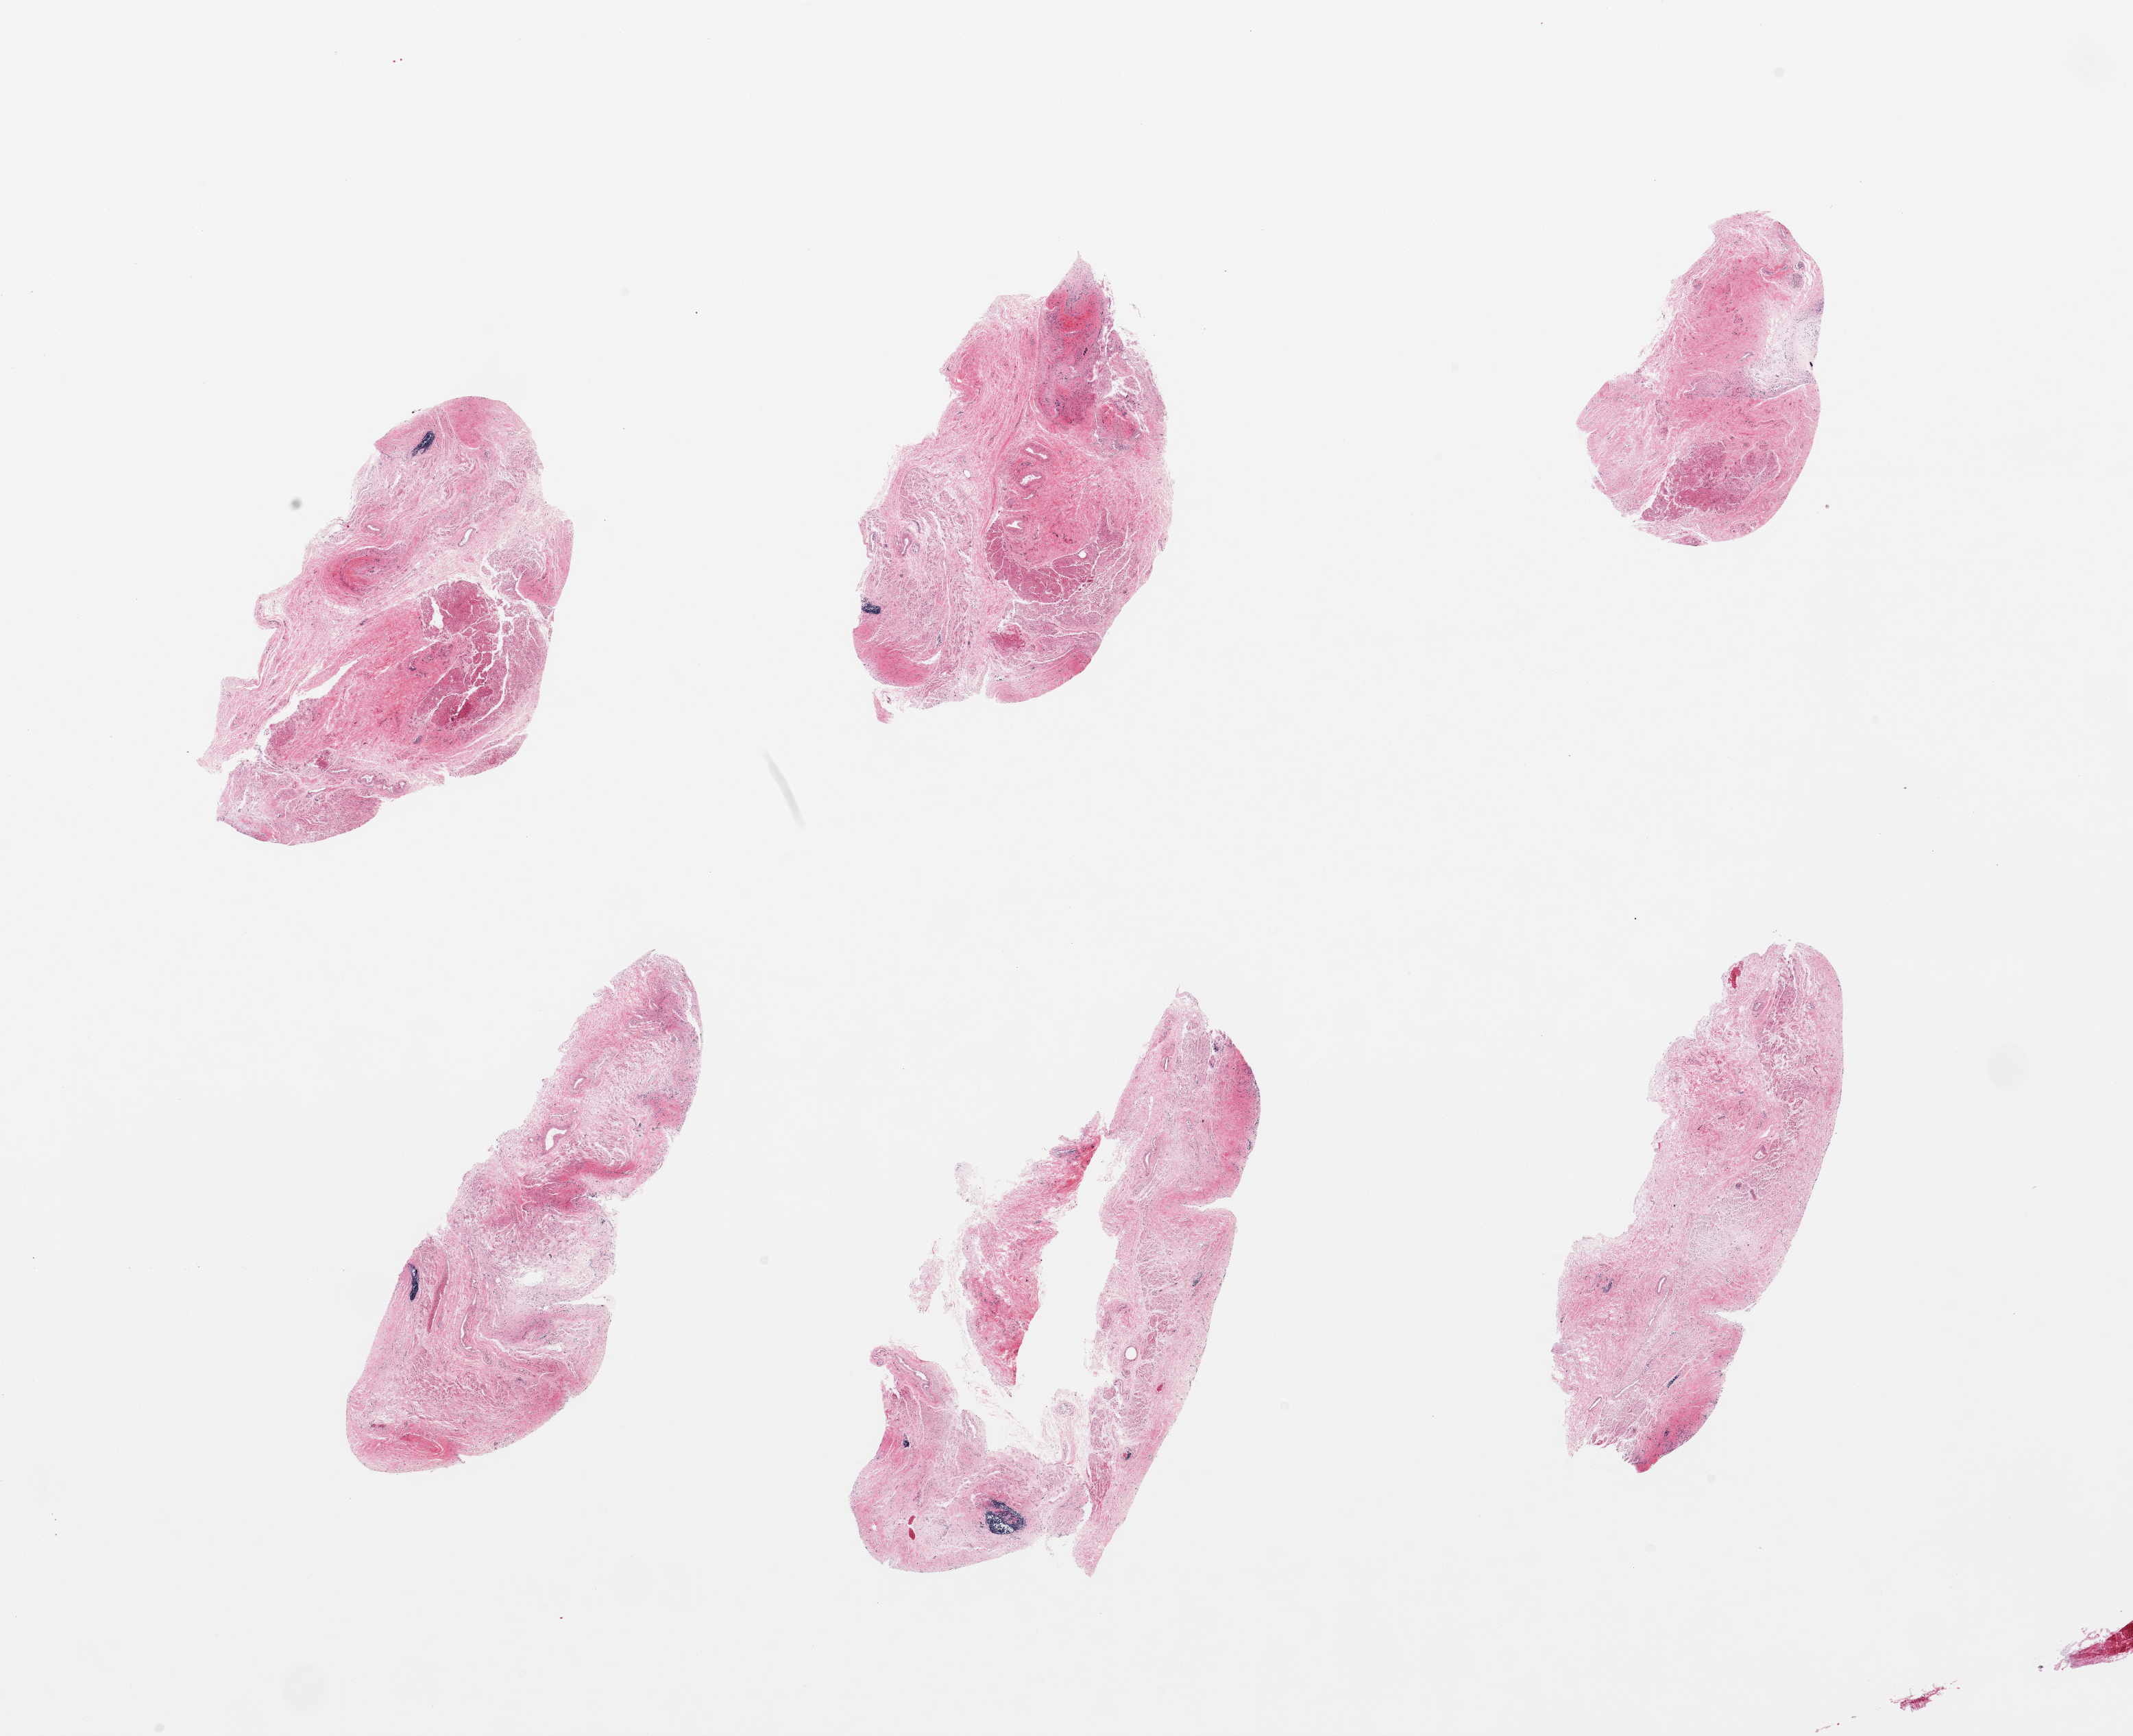
Digitized haematoxylin and eosin-stained section, brightfield — a low-resolution overview of the entire scanned area, about 24.6 x 20.0 mm (acquisition: 20x scan); PAXgene-fixed paraffin-embedded (PFPE) section; target tissue: esophageal mucous membrane; tissue donor sample. Donor: male.
Review note (as recorded): 6 pieces; no squamous epithelium.